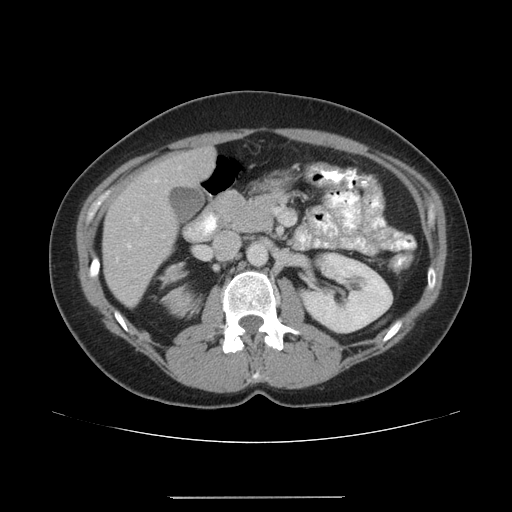
Contrast-enhanced abdominal CT, one axial slice; position 95 of 161 along the scan axis; reconstruction kernel STANDARD; intravenous contrast given; soft-tissue window (W 400 / L 40 HU); 512 × 512 image matrix, field of view 380 × 380 mm. Female patient. From the clinical record (not read from this slice): diagnosis: adrenocortical carcinoma; tumour side: right adrenal; tumour size at pathology: 9 cm; Ki-67 index: 14 %; stage (as recorded): 3.
Outlined on this slice (semi-automatically segmented with operator editing):
- mass: bounding box [x1, y1, x2, y2] px = [163, 264, 202, 319]